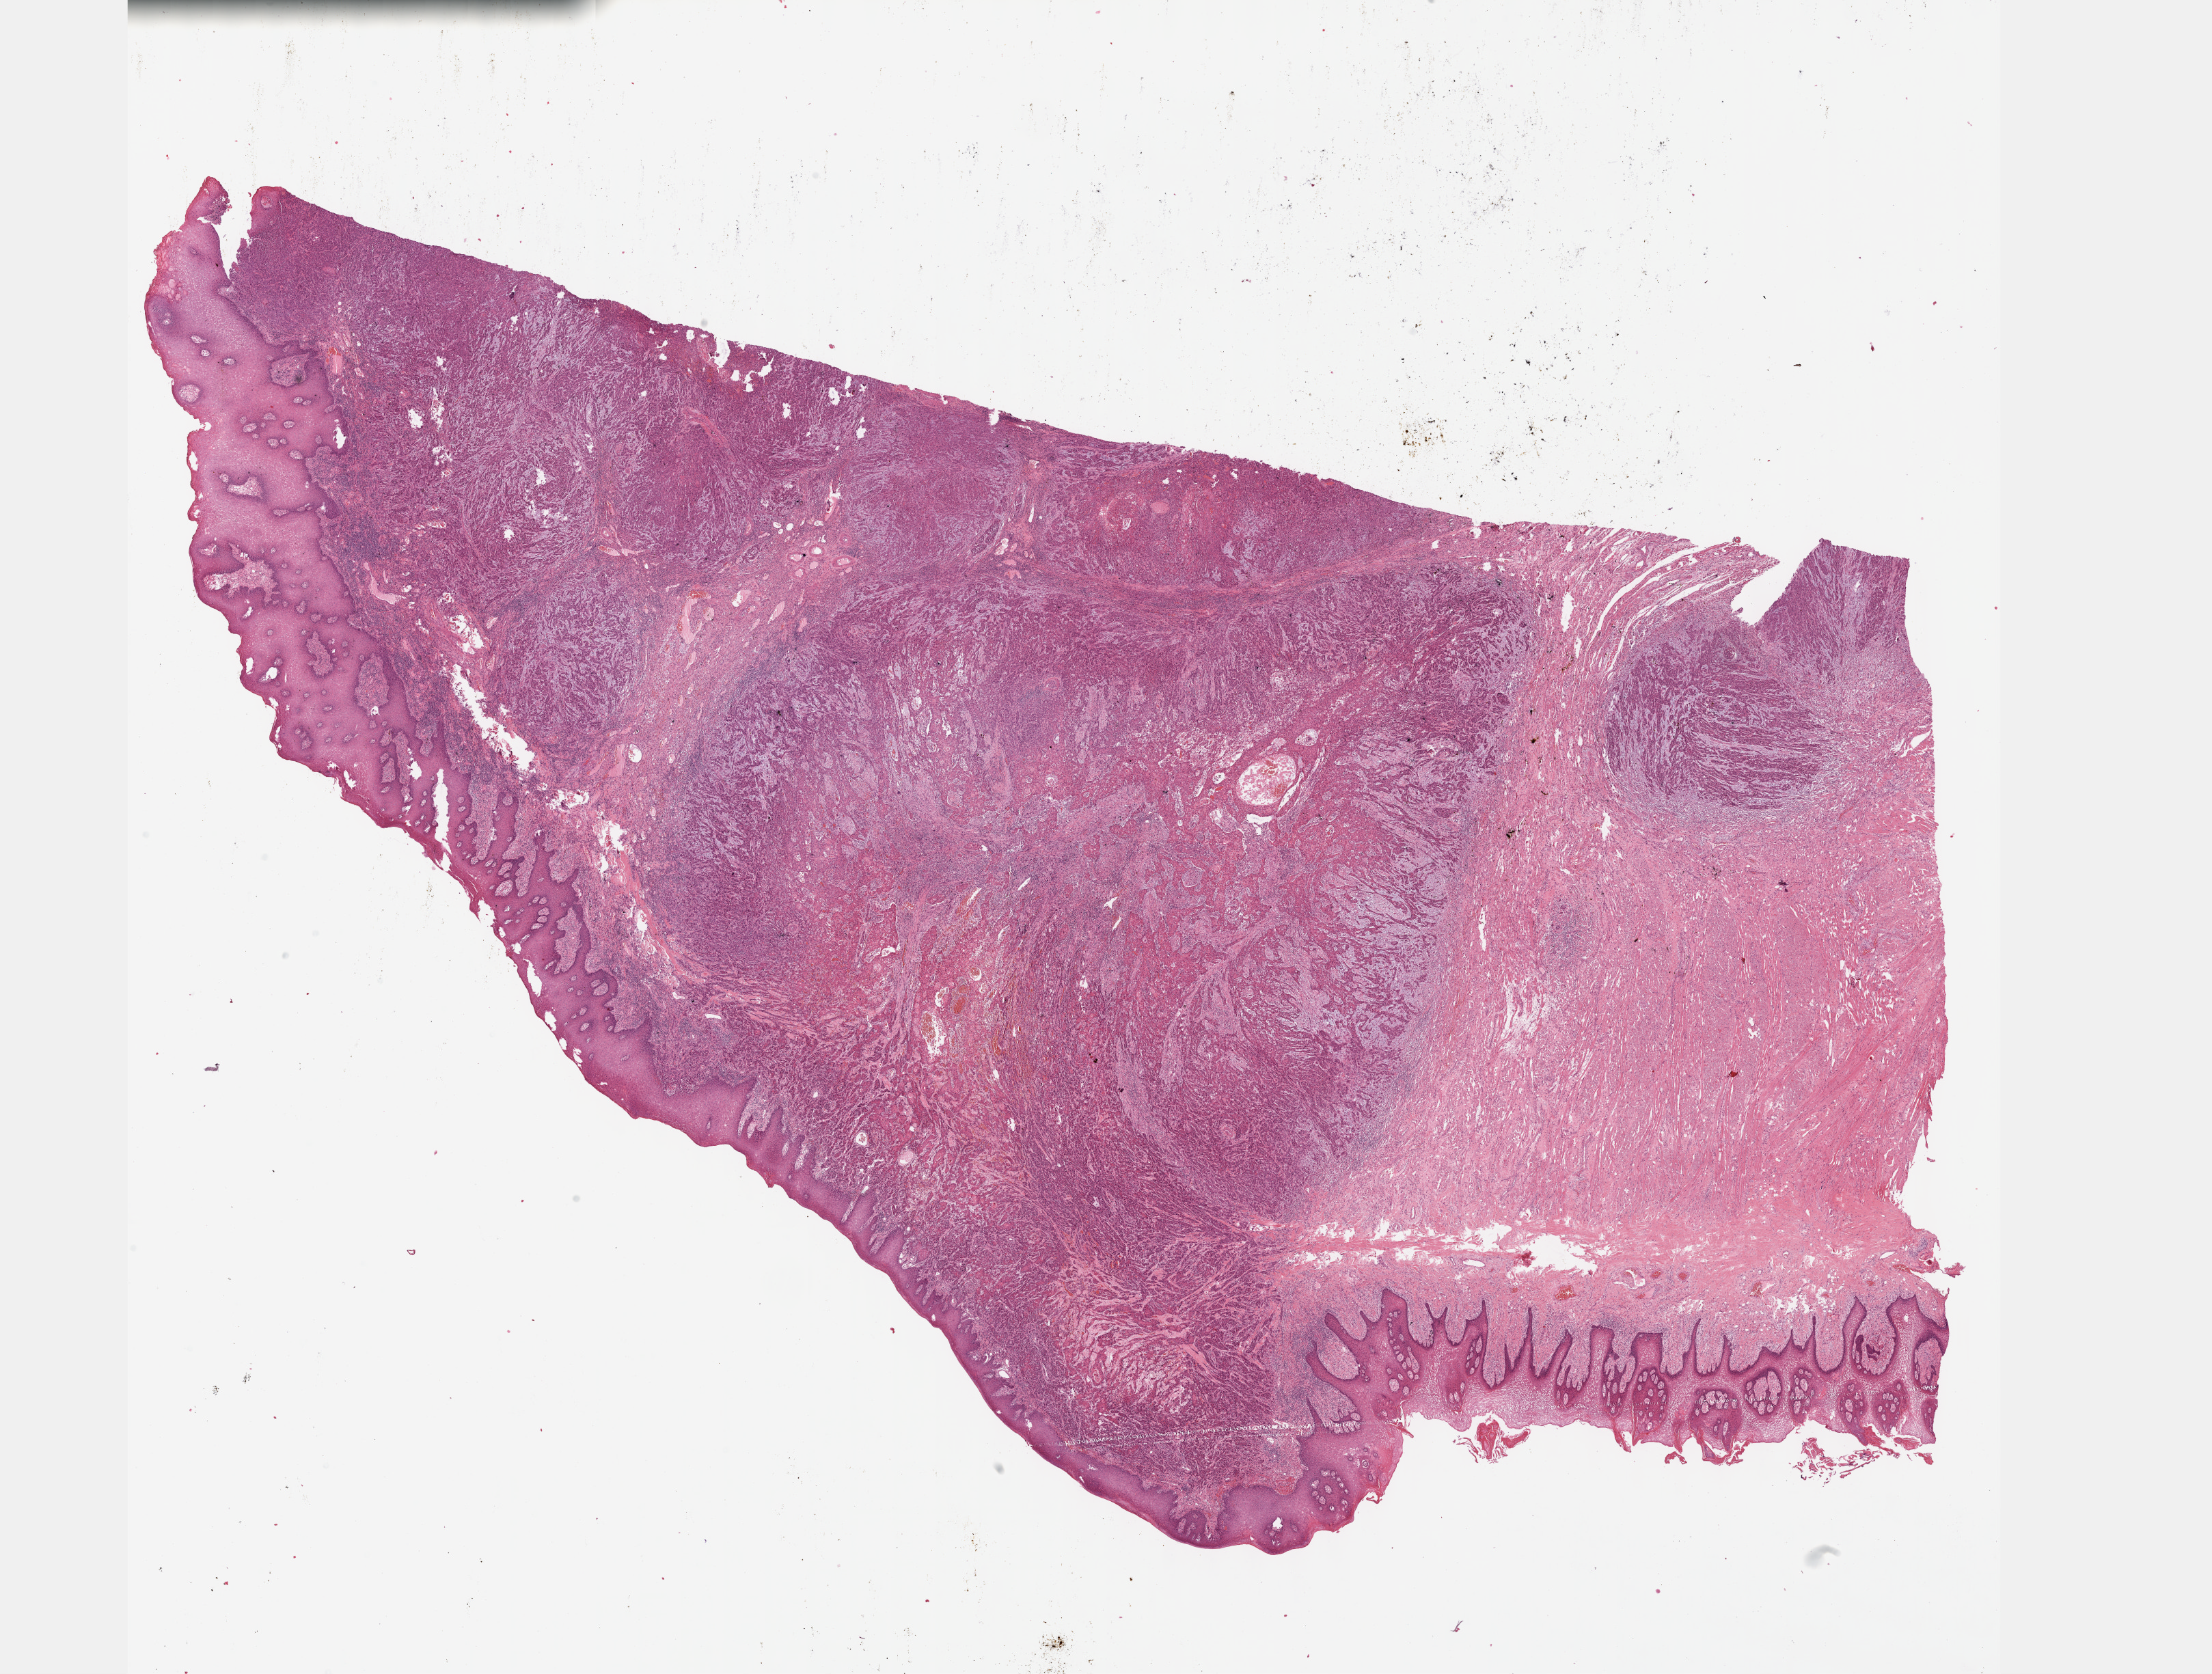
Digitized H&E-stained tissue section (whole slide) — low-resolution overview of the scanned area, about 26.2 x 19.8 mm. FFPE section. Sample: primary tumour, head and neck. Male patient; age at initial diagnosis 59 years. Histologic grade: G2 (moderately differentiated).
* AJCC pathologic stage: IVA (7th edition)
* diagnosis: Squamous cell carcinoma, NOS (tongue, NOS)
* laterality: left